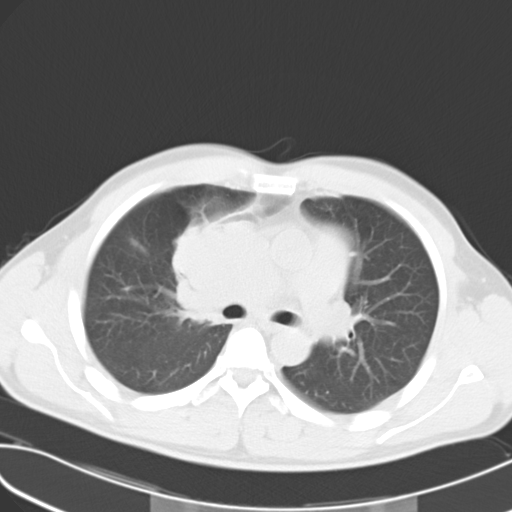
Chest CT, one axial slice. Slice 17 of 27 in the series (ordered by position). Lung window (W 1500 / L -600 HU). 512 × 512 image matrix, field of view 346 × 346 mm. Patient: male, 32 years. From the clinical record (not read from this slice): clinical TNM (as recorded): T4 N3 M0; histopathological grade: G3.
Annotated regions visible in this slice (bounding box drawn by a radiologist):
- lung tumour (recorded histology: small cell carcinoma): bounding box [x1, y1, x2, y2] px = [159, 217, 234, 333]